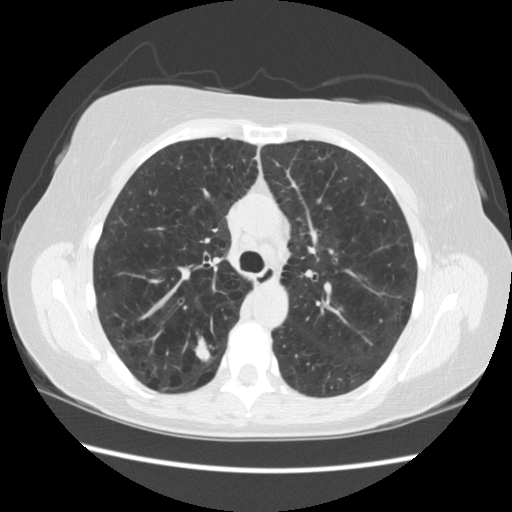
Low-dose screening chest CT, one axial slice. Slice 158 of 235 in the series (ordered by position). Reconstruction kernel STANDARD. Lung window (W 1500 / L -600 HU). 2.5 mm slice thickness. 512 × 512 image matrix, field of view 360 × 360 mm.
Outlined on this slice (outlined manually by an expert reader):
- lesion 1 (tumor, upper lobe of right lung): bounding box [x1, y1, x2, y2] px = [196, 347, 210, 359]